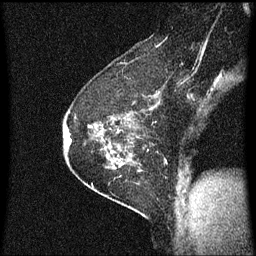
Breast MRI (dynamic contrast-enhanced), one sagittal slice. Slice 44 of 60 in the series (ordered by position). Dynamic contrast-enhanced series, image 2 of 3 at this slice position (ordered by acquisition). 1.5 T. TE 4.2 ms, TR 8.4 ms. 2 mm slice thickness. 256 × 256 image matrix, field of view 200 × 200 mm. Female patient, age 60 years.
Annotated regions visible in this slice (semi-automatic segmentation, software-assisted and operator-edited):
- analysis volume of interest (the breast-tissue region the enhancement analysis was run in; not a lesion): bounding box <69,66,146,193> (left, top, right, bottom; pixels)
- tumour enhancement mask (voxels above the 70 % enhancement threshold inside the analysis volume of interest): <69,124,135,165>